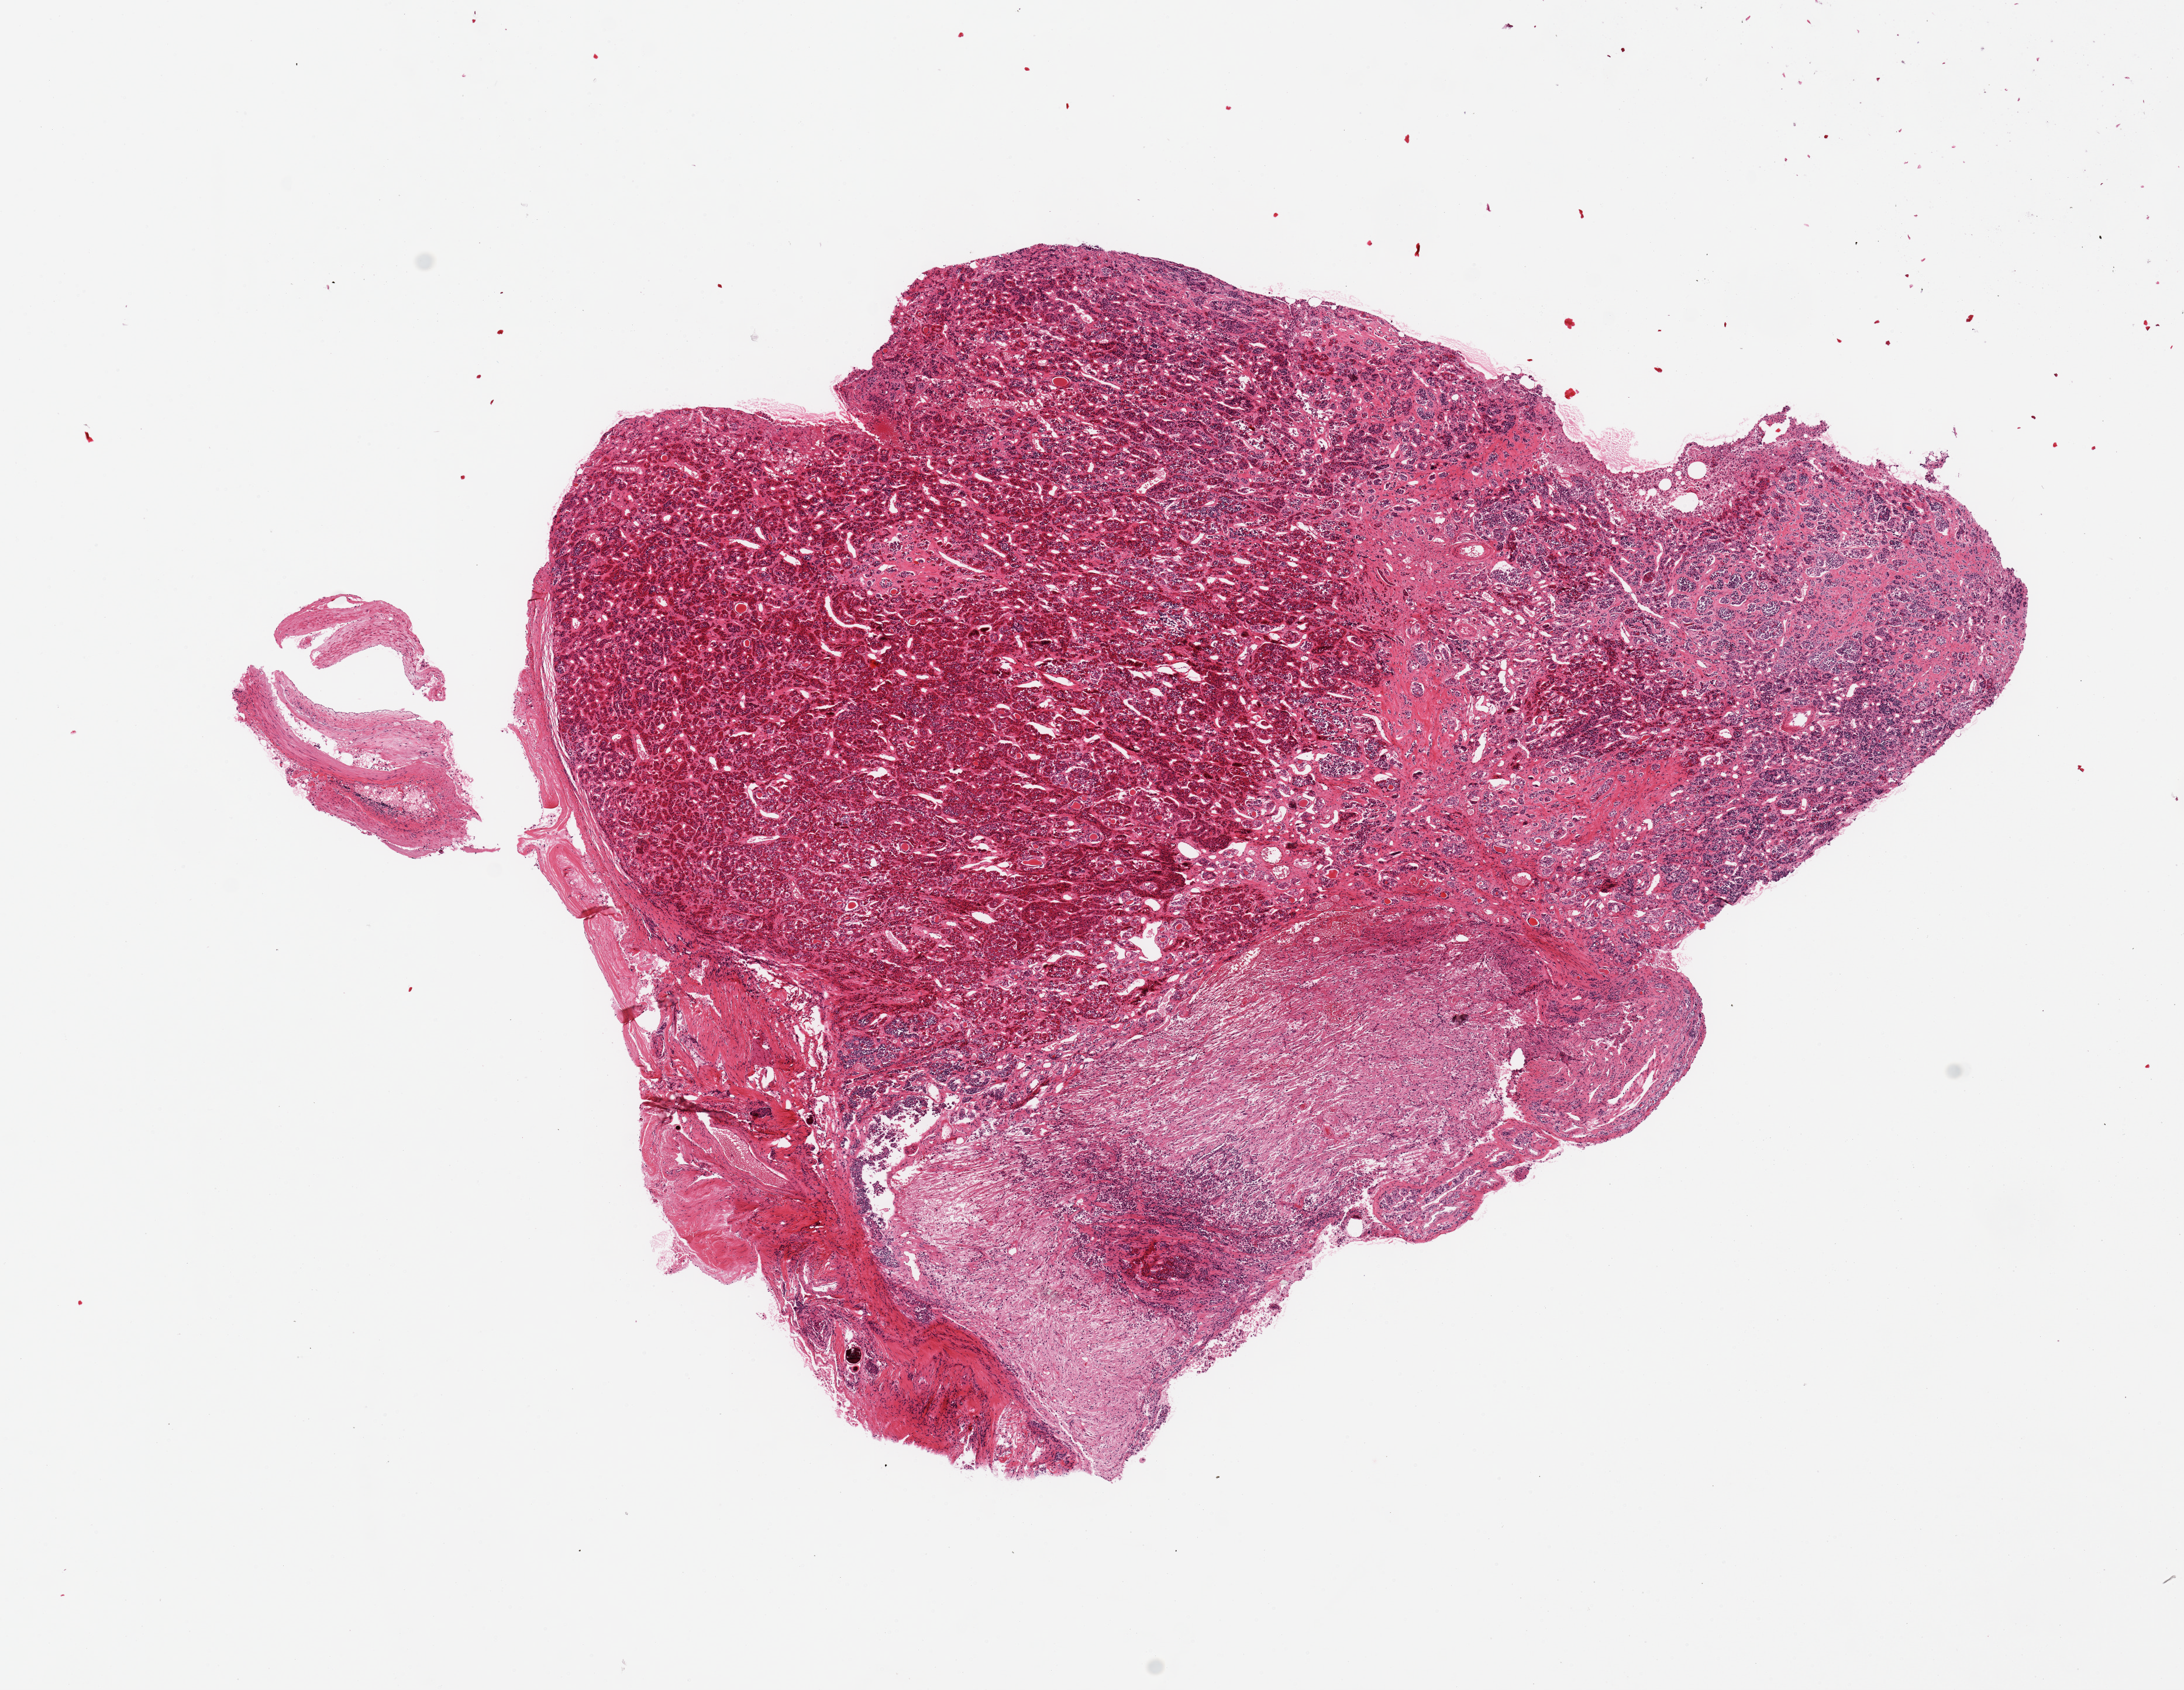
Whole-slide image, H&E stain — a low-resolution overview of the entire scanned area, about 14.8 x 11.4 mm (slide scanned at 20x), PAXgene-fixed paraffin-embedded (PFPE) section, target tissue: pituitary, donor tissue sample. Female donor.
Reviewer comment on this tissue sample: 1 piece, mainly adenohypophysis; 5x2mm nubbin of neurohypophysis attached.